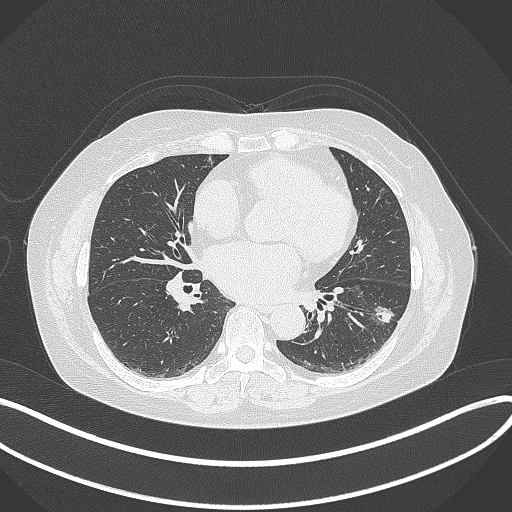
Chest CT, one axial slice. Position 164 of 373 along the scan axis. 120 kVp. Lung window (W 1500 / L -600 HU). 1 mm slice thickness. 512 × 512 image matrix, field of view 400 × 400 mm. Female patient, age 67 years. From the clinical record (not read from this slice): clinical TNM (as recorded): T1c N0 M0; histopathological grade: G2.
Annotated regions visible in this slice (bounding box drawn by a radiologist):
- lung tumour (recorded histology: adenocarcinoma): bounding box [x1, y1, x2, y2] px = [368, 298, 398, 330]